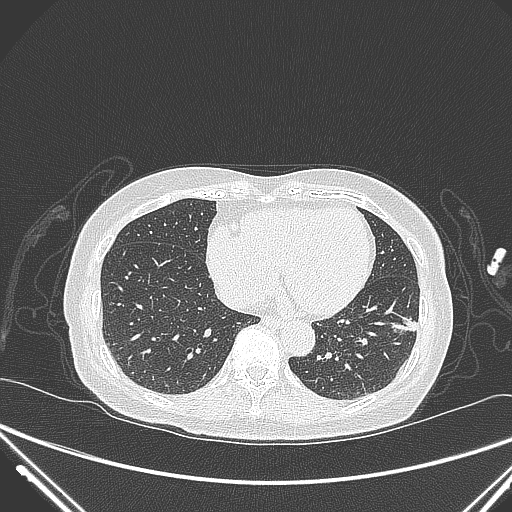
Chest CT, one axial slice. Position 103 of 310 along the scan axis. Lung window (W 1500 / L -600 HU). 1 mm slice thickness. 512 × 512 image matrix, field of view 377 × 377 mm. Patient: female, 82 years. From the clinical record (not read from this slice): clinical TNM (as recorded): T1c N0 M0.
Annotated regions visible in this slice (rectangle marked by the reading radiologist):
- lung tumour (recorded histology: adenocarcinoma): bounding box (x1, y1, x2, y2) in pixels: (385, 304, 417, 335)